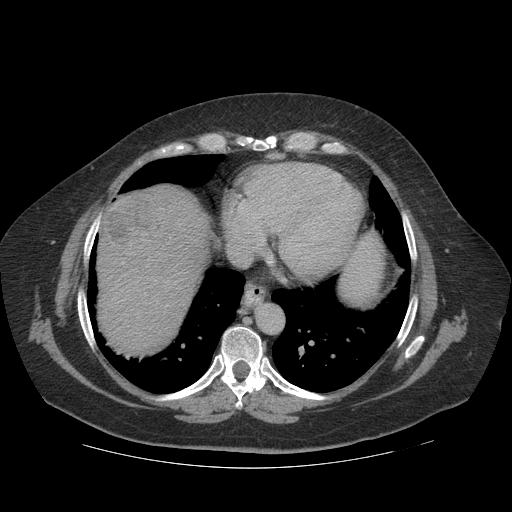
Contrast-enhanced abdominal CT (liver protocol), one axial slice; position 104 of 121 along the scan axis; 140 kVp; soft-tissue window (W 400 / L 40 HU); 2.5 mm slice thickness; 512 × 512 image matrix, field of view 420 × 420 mm. From the clinical record (not read from this slice): diagnosis: hepatocellular carcinoma (patient treated with transarterial chemoembolisation; whether this scan precedes or follows treatment is not stated here); TNM stage (as recorded): Stage-IIIA; Child-Pugh class: A; tumour differentiation: well differentiated; tumour nodularity: multinodular.
Outlined on this slice (semi-automatic segmentation, software-assisted and operator-edited):
- liver parenchyma outside the tumour (the mass and vessels are separate outlines, so this box may not span the whole liver): bounding box (x1, y1, x2, y2) in pixels: (96, 184, 208, 352)
- mass: (100, 197, 159, 245)